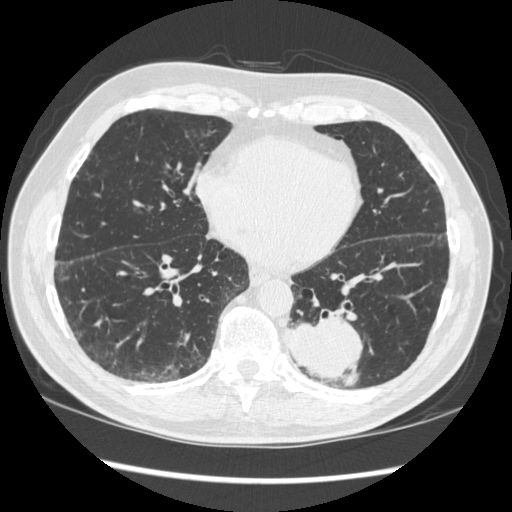
Low-dose screening chest CT, axial slice, baseline screening round, lung window (W 1500 / L -600 HU), 1.25 mm slice thickness, standard (soft-tissue) reconstruction kernel (STANDARD), slice 123 of 348 in the series, 512 × 512 image matrix, field of view 360 × 360 mm. Male participant, aged 72 years at enrolment.
Expert reader's lesion annotation, bounding box <273,297,377,386> (left, top, right, bottom; pixels). The screening reader recorded 2 non-calcified nodules or masses ≥4 mm on this exam; which of them this box marks is not recorded. Official screen result: positive, change unspecified: nodule(s) >= 4 mm or enlarging nodule(s), mass(es), or other non-specific abnormalities suspicious for lung cancer. Participant outcome: lung cancer diagnosed 37 days after this screen — squamous cell carcinoma, NOS, left lower lobe, stage IIIA (AJCC 6th edition), 60 mm at pathology.